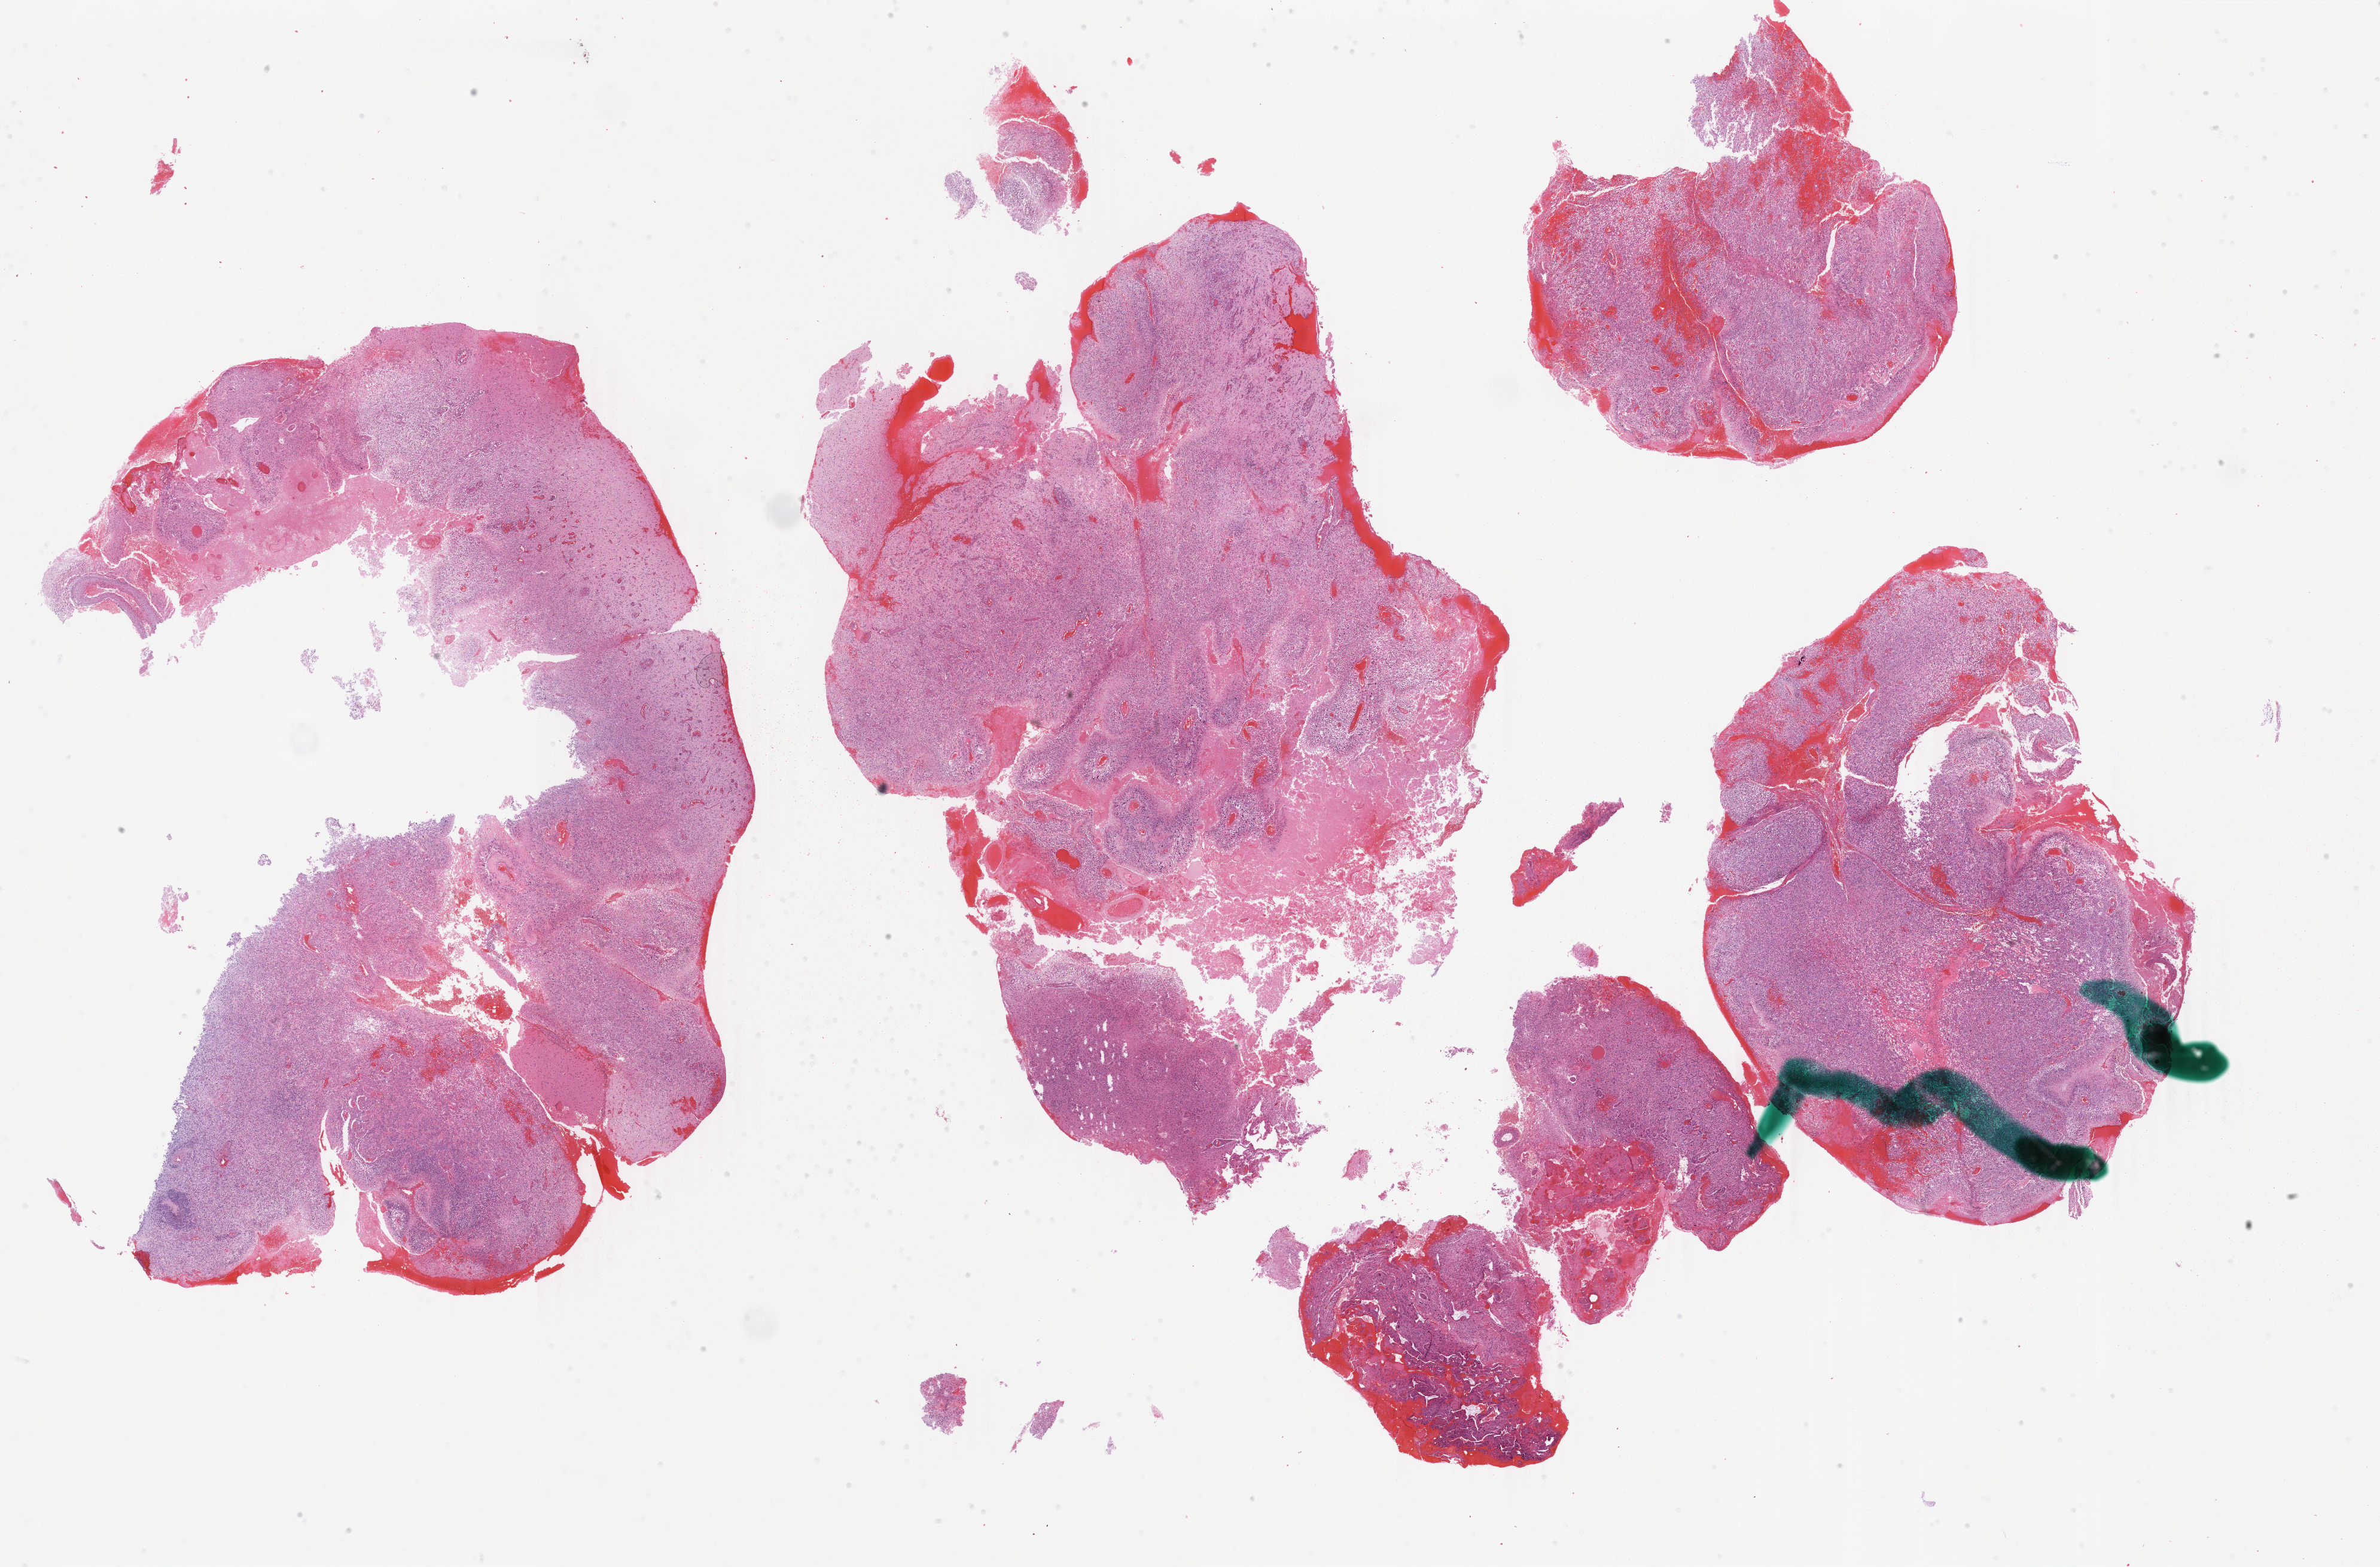
Digitized H&E-stained tissue section (whole slide) — shown as a low-resolution overview of the whole scanned area (about 31.6 x 20.8 mm). Formalin-fixed paraffin-embedded (FFPE) diagnostic section. Brain, primary tumour sample. Male, age 74 years at initial diagnosis.
- histologic diagnosis: Glioblastoma